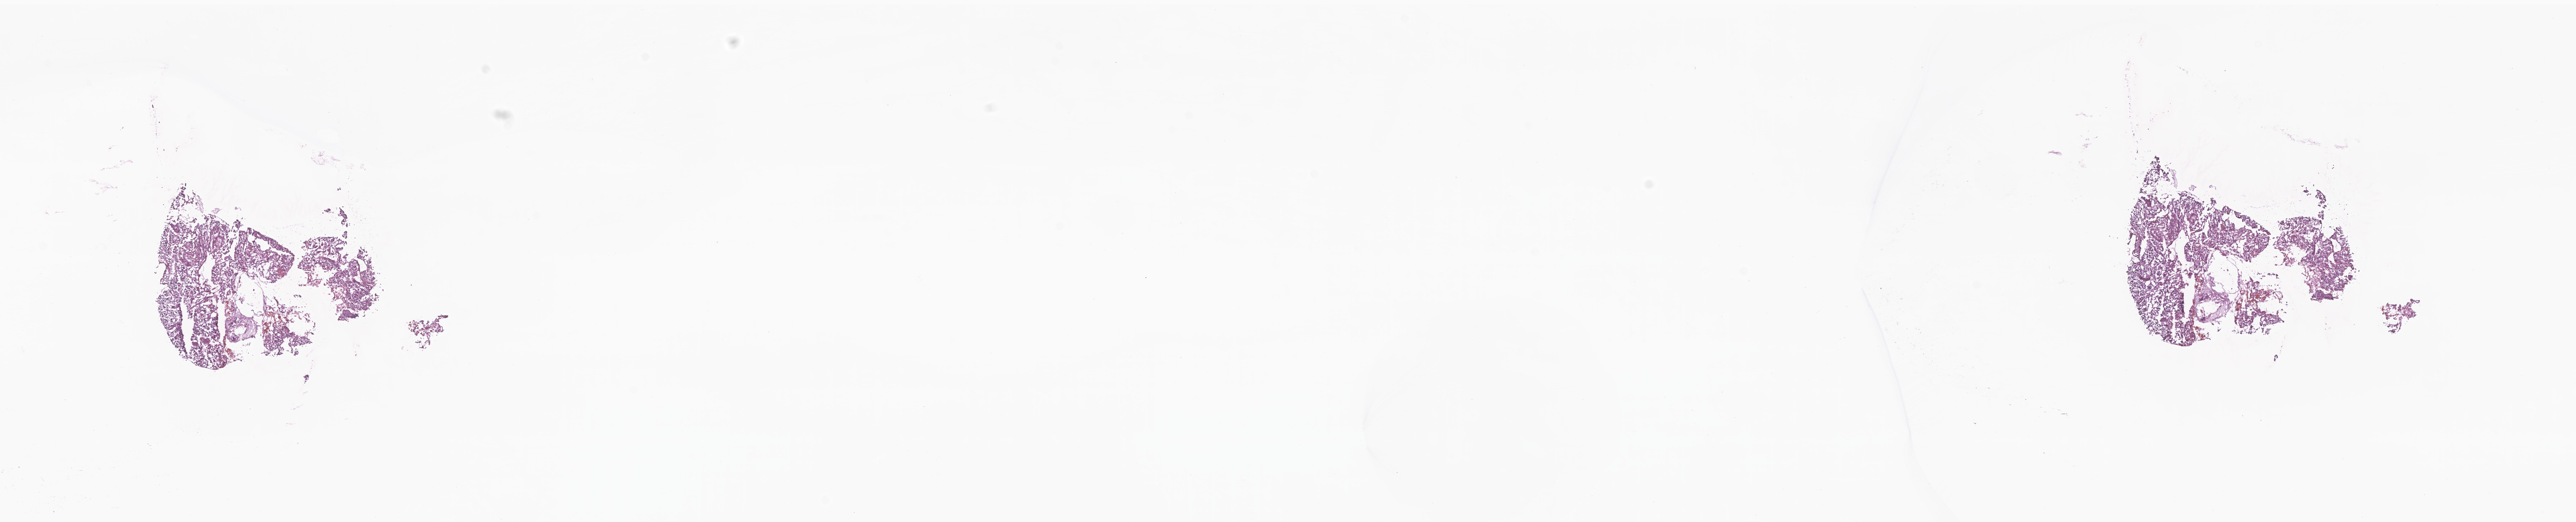
Digitized haematoxylin and eosin-stained section of tumor tissue from the frontal lobe — shown as a low-resolution overview of the whole scanned area (about 30.3 x 6.2 mm), frozen section (OCT-embedded). Patient female; age 211 months (17 years 7 months).
* diagnosis (ICD-O-3 morphology term): Glioma, malignant